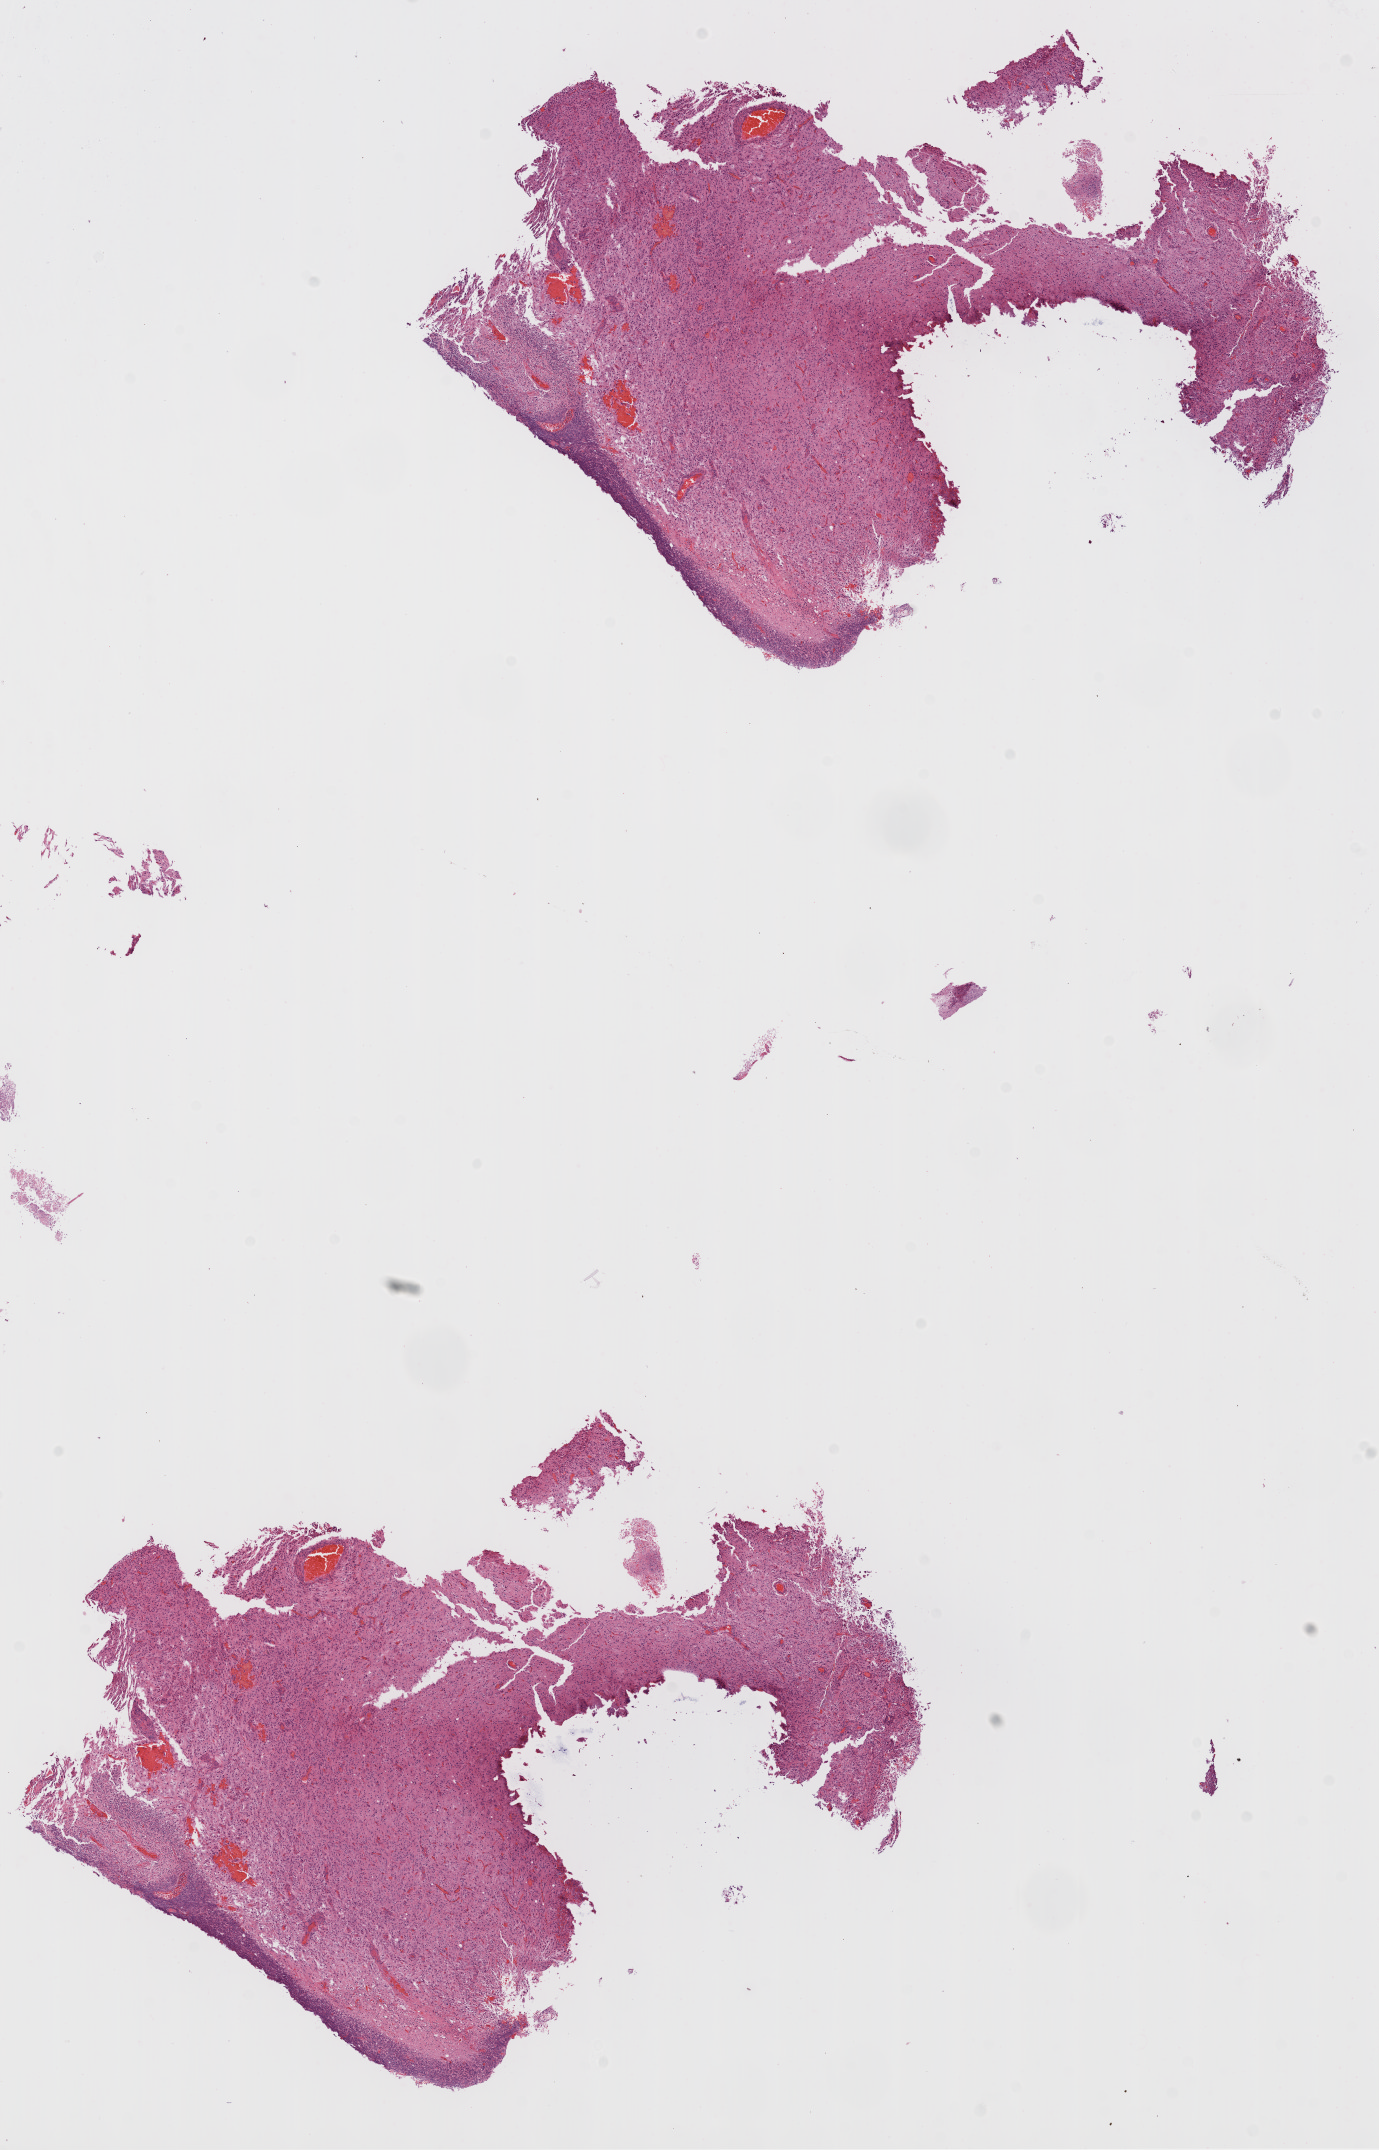
Whole-slide histology image, H&E, shown as a low-resolution overview of the whole scanned area (about 11.1 x 17.3 mm), formalin-fixed paraffin-embedded (FFPE) diagnostic section, primary tumour sample from the brain. Patient: male, age at initial diagnosis 62 years.
• histologic diagnosis: Glioblastoma